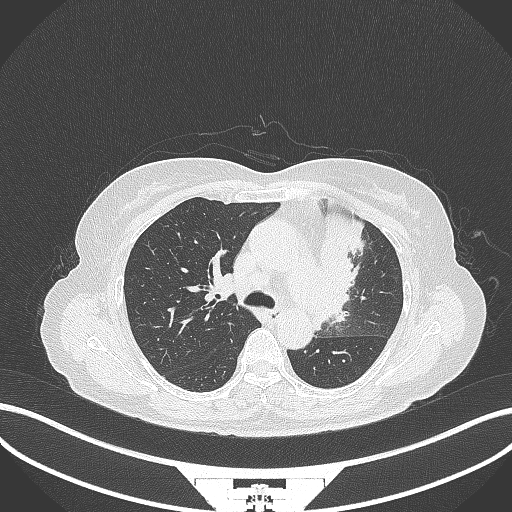
Chest CT, one axial slice; position 221 of 382 along the scan axis; reconstruction kernel B70f; 120 kVp; lung window (W 1500 / L -600 HU); 512 × 512 image matrix, field of view 400 × 400 mm. Female patient, age 64 years. Case-level facts recorded for this patient, not image findings: clinical TNM (as recorded): T2a N2 M0.
Outlined on this slice (rectangle marked by the reading radiologist):
- lung tumour (recorded histology: adenocarcinoma): box from (x=314, y=201) to (x=369, y=333) px